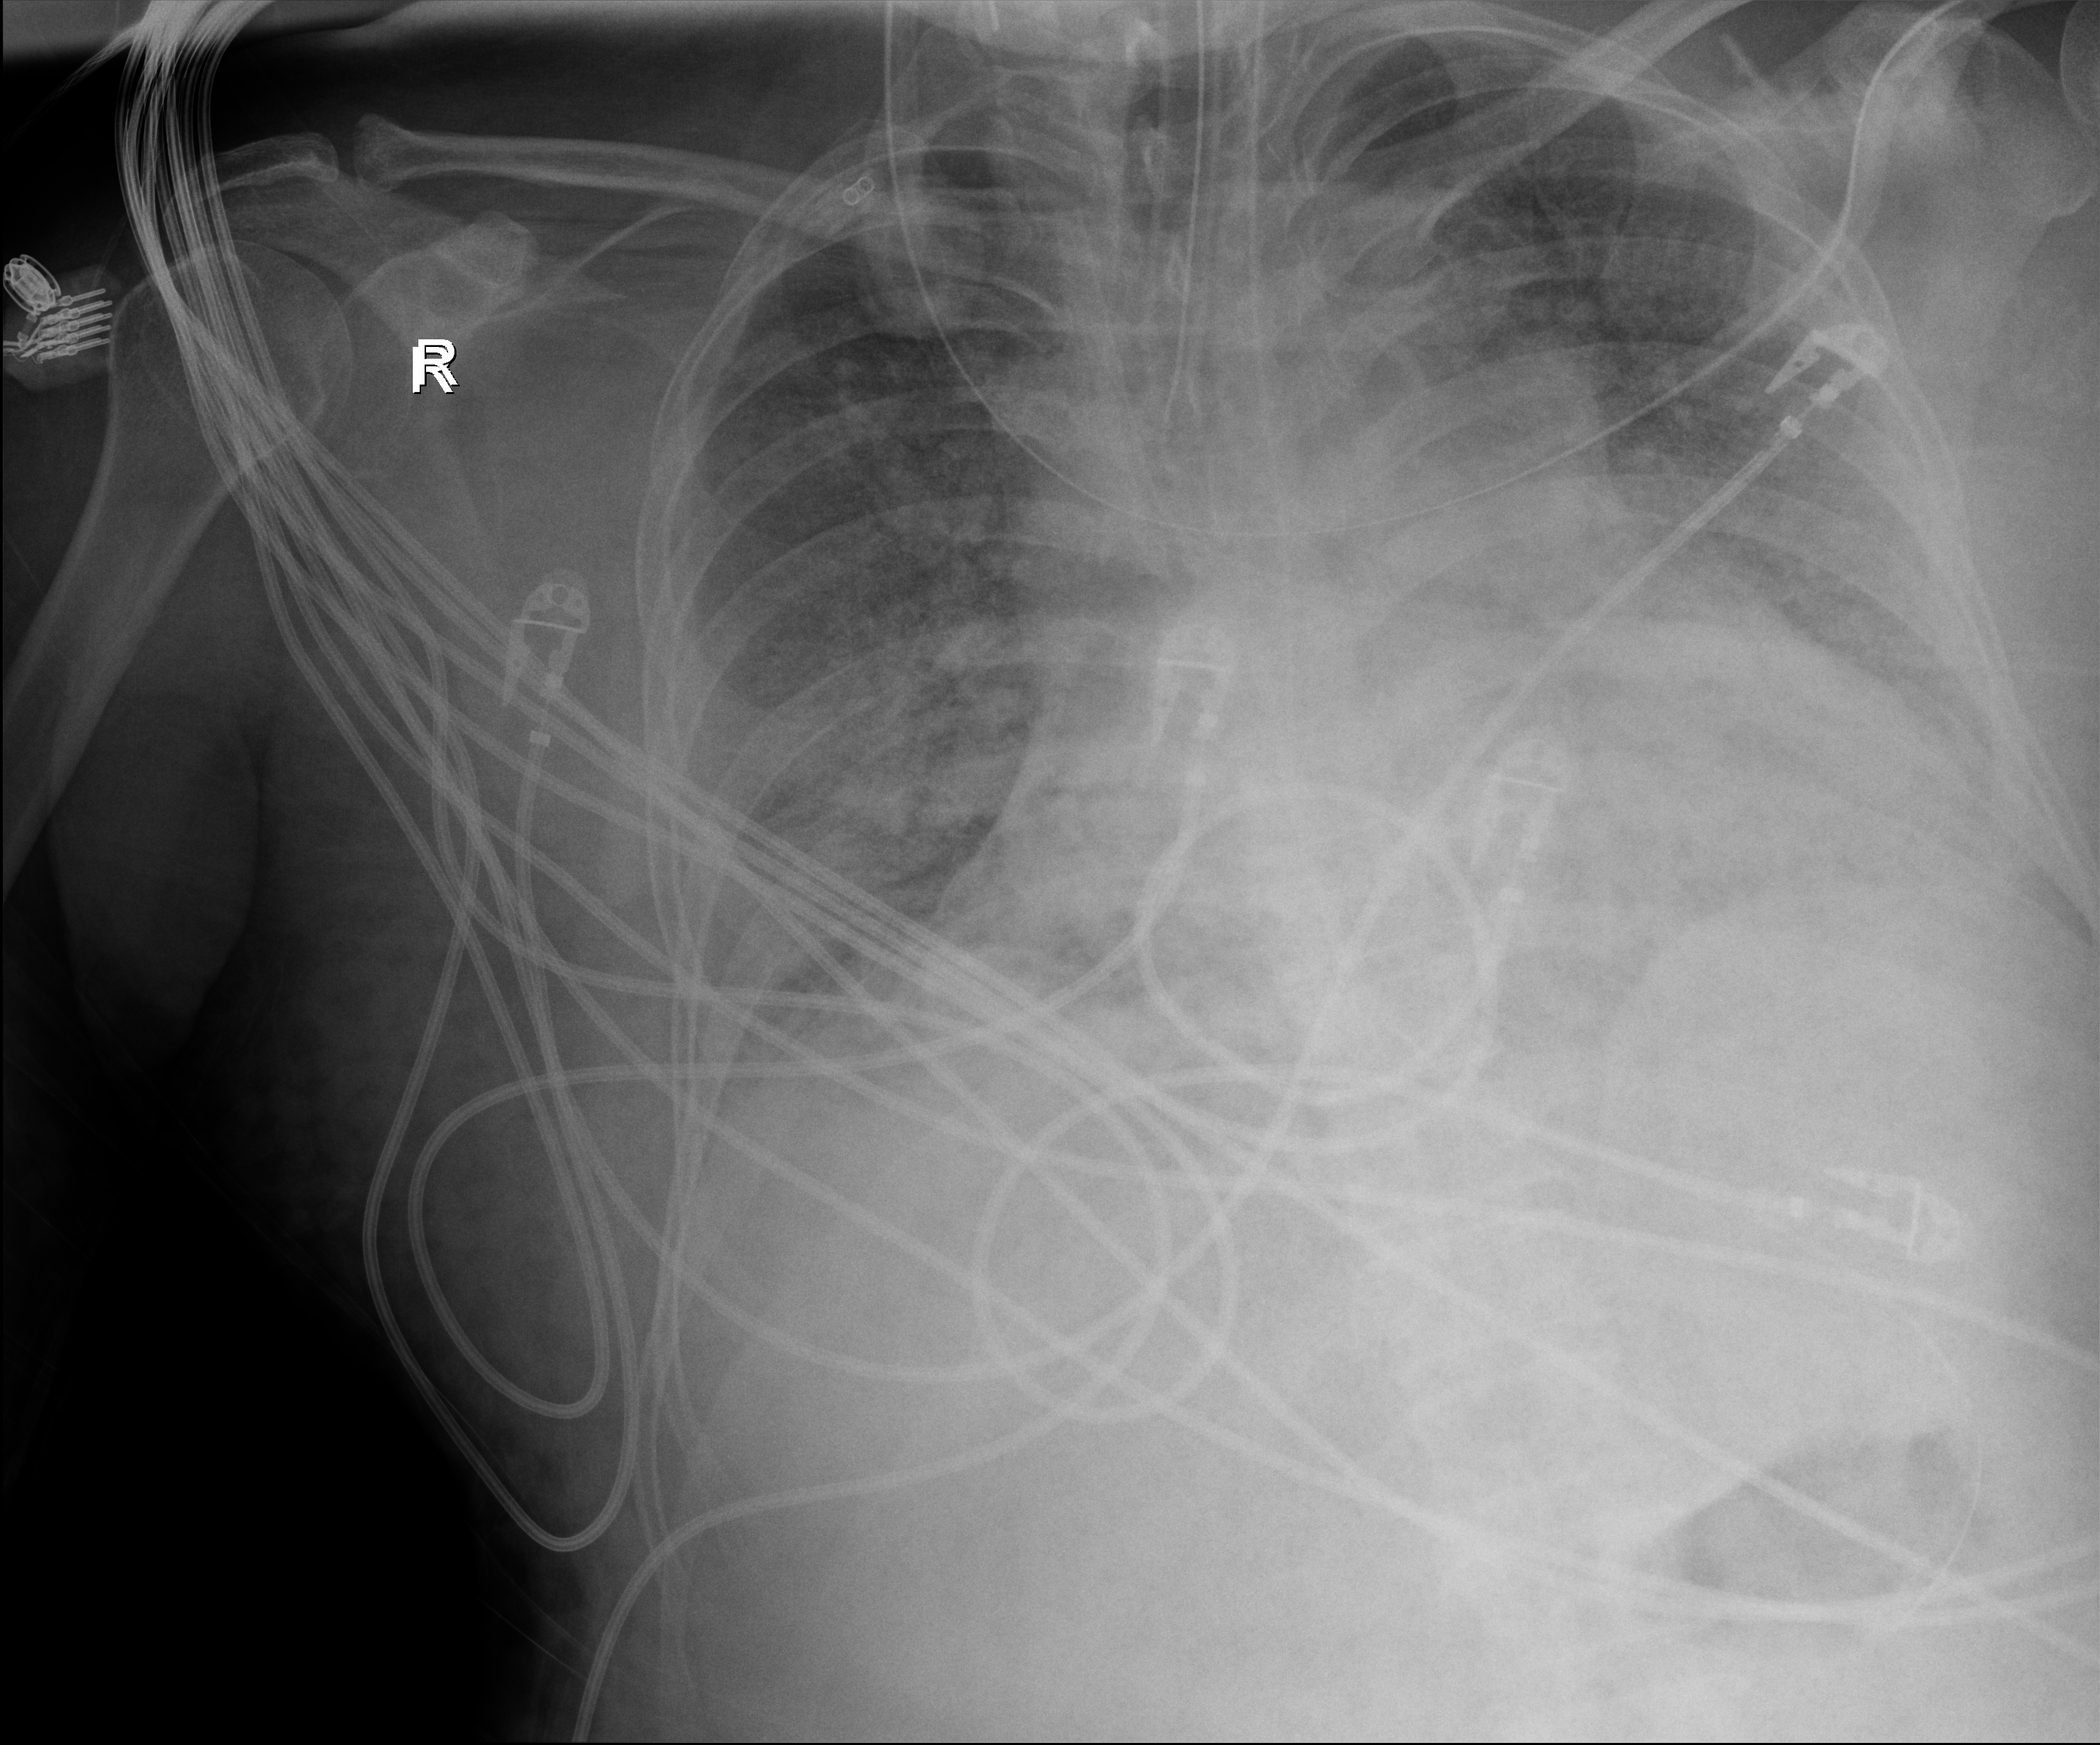
Chest X-ray (portable). Patient hospitalised with COVID-19, aged 18–59 years.
Hospital-stay facts (about this admission, not read from this image; timing relative to this image not recorded): COPD (admission record): no.